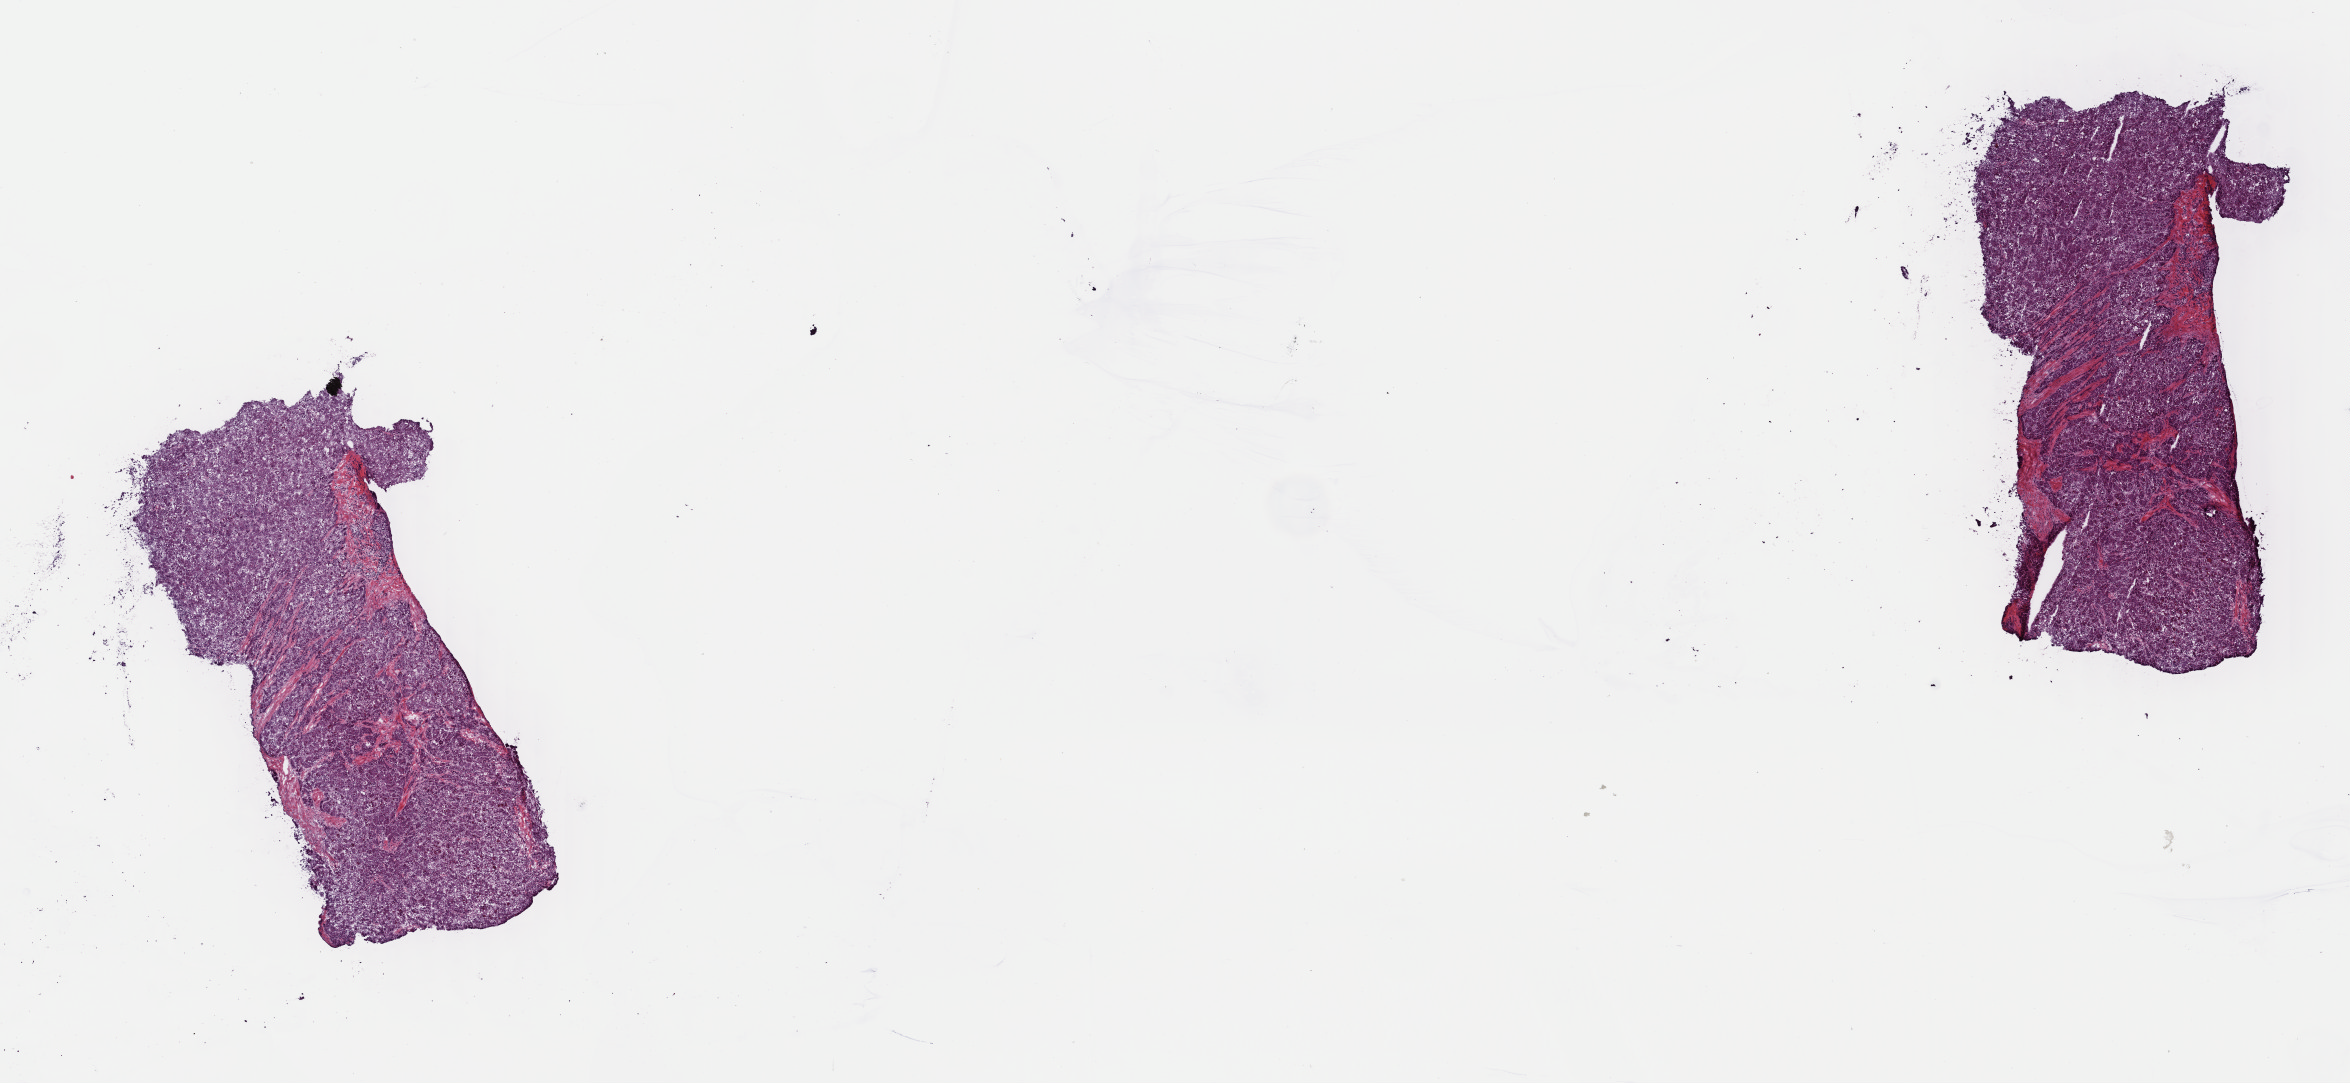
Digitized H&E tissue section (whole slide), a low-resolution overview of the entire scanned area, about 18.5 x 8.5 mm; frozen section; liver, primary tumour sample. Patient: male, age at initial diagnosis 62 years. Slide review estimates, as recorded: tumour cells 73%, tumour nuclei 85%.
Diagnosis: Hepatocellular carcinoma, NOS.